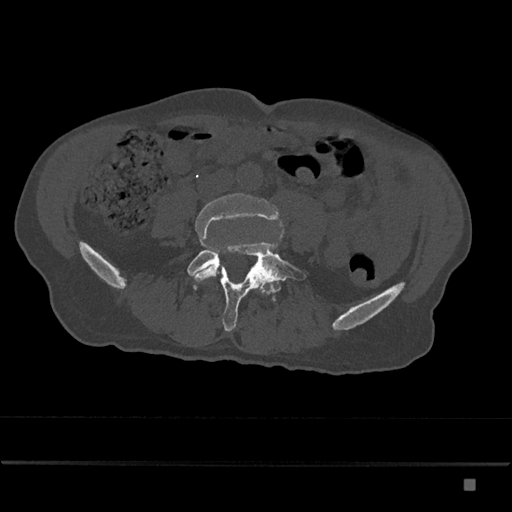
CT including the spine, one axial slice; position 299 of 797 along the scan axis; 120 kVp; bone window (W 1800 / L 400 HU); 512 × 512 image matrix, field of view 390 × 390 mm. Patient: male, 72 years. Case-level facts recorded for this patient, not image findings: primary cancer: prostate.
Outlined on this slice (semi-automatically segmented with operator editing):
- L4 vertebra: box from (x=191, y=193) to (x=282, y=282) px
- L5 vertebra: (x=187, y=241)–(x=307, y=332)